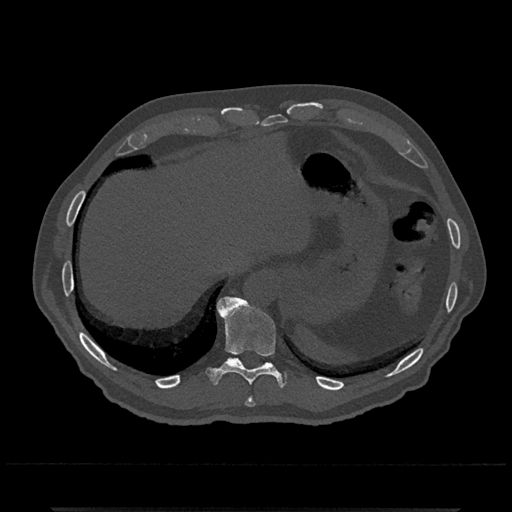
CT including the spine, one axial slice; position 550 of 797 along the scan axis; reconstruction kernel Br40s/3; 120 kVp; bone window (W 1800 / L 400 HU); 512 × 512 image matrix, field of view 393 × 393 mm. Male patient, age 67 years. From the clinical record (not read from this slice): primary cancer: prostate.
Outlined on this slice (semi-automatic segmentation, software-assisted and operator-edited):
- T10 vertebra: bounding box [x1, y1, x2, y2] px = [207, 296, 284, 387]
- T11 vertebra: [227, 357, 241, 362]
- T9 vertebra: [245, 397, 256, 407]